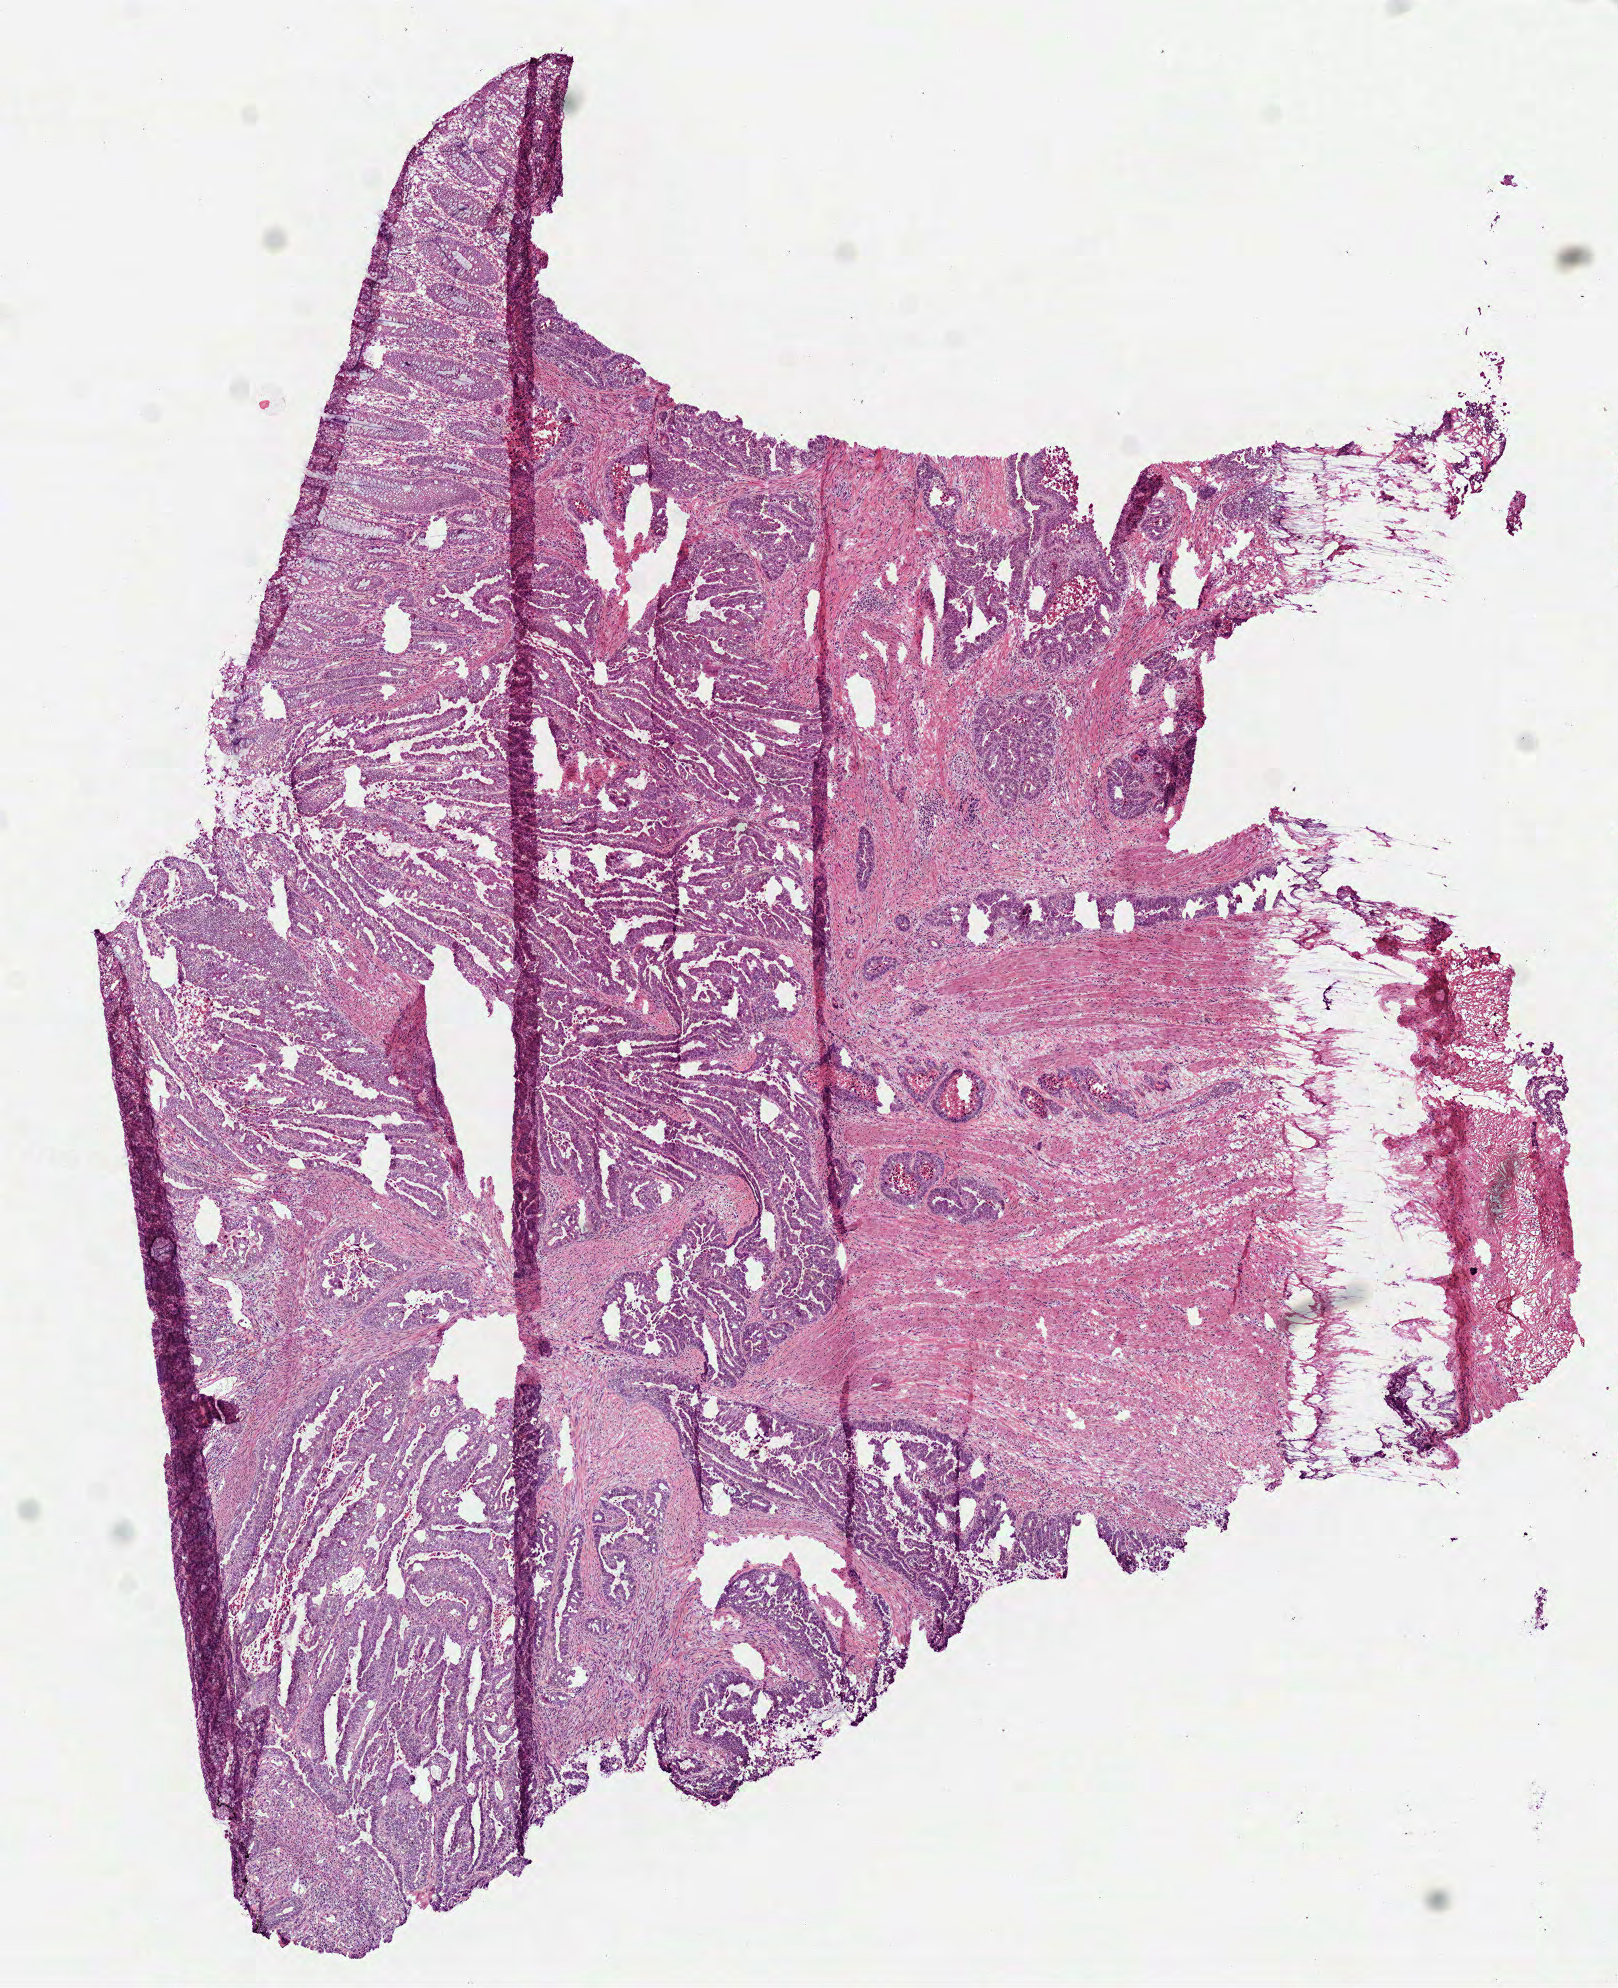
Digitized H&E tissue section (whole slide) — whole scanned area (about 6.5 x 8.0 mm) shown as a low-resolution overview. Frozen section from the bottom of the tissue portion. Primary tumour sample from the colon. Patient: male, age at initial diagnosis 66 years. Slide review estimates, as recorded: tumour cells 80%, tumour nuclei 72%, normal cells 10%, stromal cells 0%, necrosis 10%. Infiltration values recorded for this section: lymphocyte infiltration 7%, monocyte infiltration 8%, neutrophil infiltration 7%.
TNM: T3 N1b M0. Pathologic diagnosis: Adenocarcinoma, NOS (ascending colon). AJCC pathologic stage: IIIB.